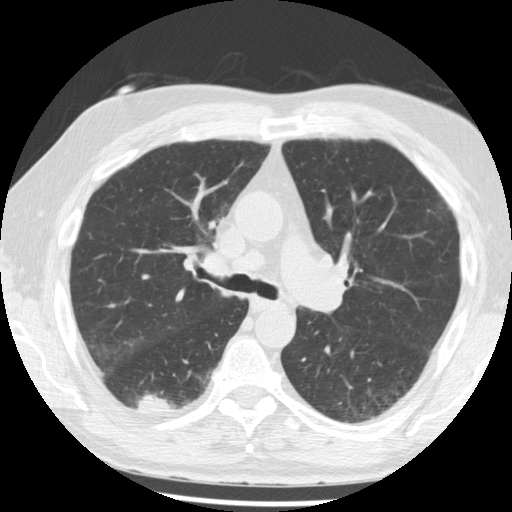
Low-dose screening chest CT, one axial slice. Position 133 of 221 along the scan axis. 120 kVp. Lung window (W 1500 / L -600 HU). 512 × 512 image matrix, field of view 350 × 350 mm.
Annotated regions visible in this slice (outlined manually by an expert reader):
- lesion 1 (tumor, lower lobe of right lung): box from (x=137, y=395) to (x=176, y=413) px